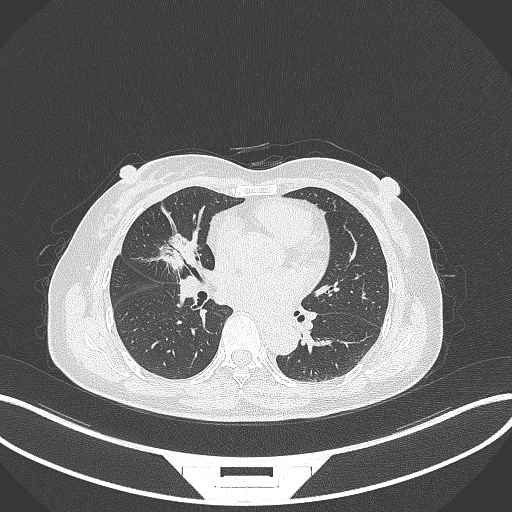
Chest CT, one axial slice; slice 146 of 284 in the series (ordered by position); reconstruction kernel B70f; lung window (W 1500 / L -600 HU); 1 mm slice thickness; 512 × 512 image matrix, field of view 400 × 400 mm. Patient: female, 51 years. Case-level facts recorded for this patient, not image findings: clinical TNM (as recorded): T1c N0 M0; histopathological grade: G2.
Annotated regions visible in this slice (rectangle marked by the reading radiologist):
- lung tumour (recorded histology: adenocarcinoma): bounding box <158,232,203,273> (left, top, right, bottom; pixels)